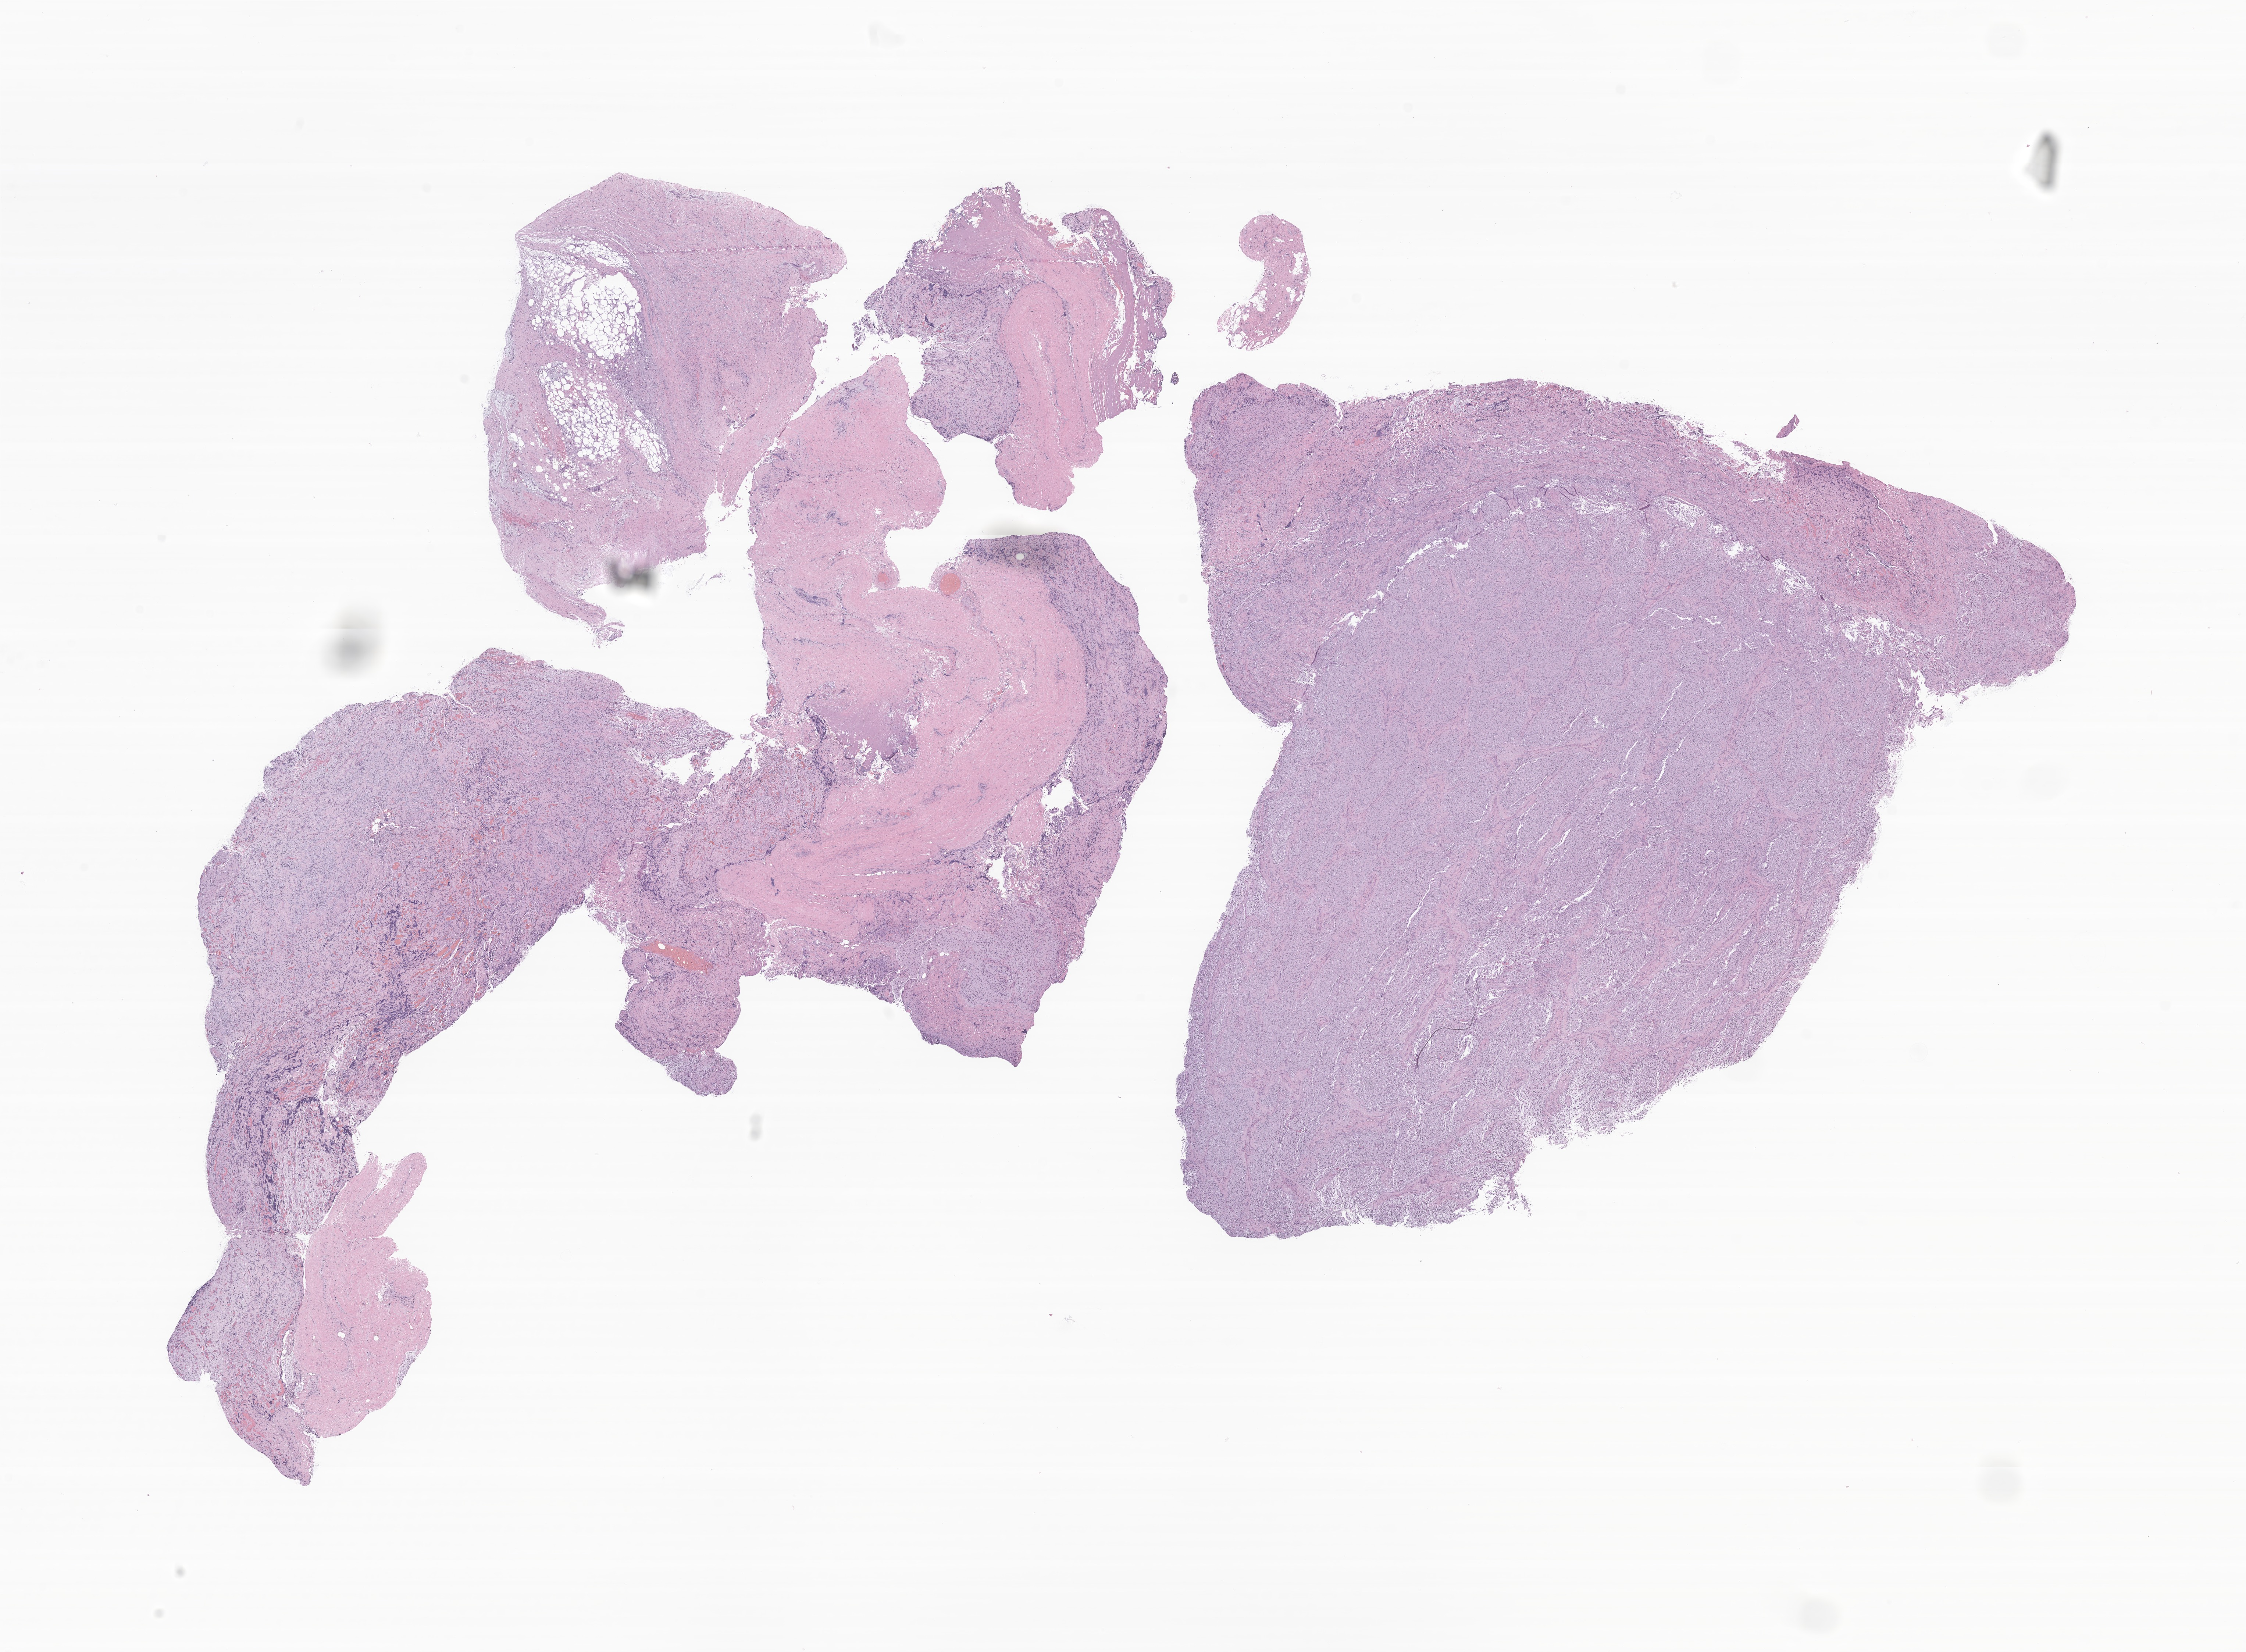
Whole-slide image, haematoxylin and eosin stain of tumor tissue from the eye, shown as a low-resolution overview of the whole scanned area (about 25.8 x 18.9 mm); FFPE section. Patient male; age 64 months (5 years 4 months).
• diagnosis: Neoplasm, uncertain whether benign or malignant